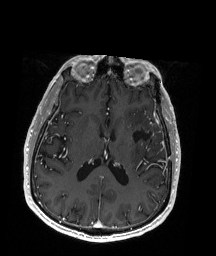
Brain MRI from a brain-tumour surgery series, one axial slice; slice 87 of 192 in the series (ordered by position); T1-weighted post-contrast; 1 mm slice thickness; 216 × 256 image matrix, field of view 211 × 250 mm. From the clinical record (not read from this slice): histopathology: Oligodendroglioma; WHO grade: 2; IDH mutation: yes; tumour location: Left Insular.
Annotated regions visible in this slice (manually delineated by an expert):
- previous resection cavity: bounding box <132,126,163,140> (left, top, right, bottom; pixels)